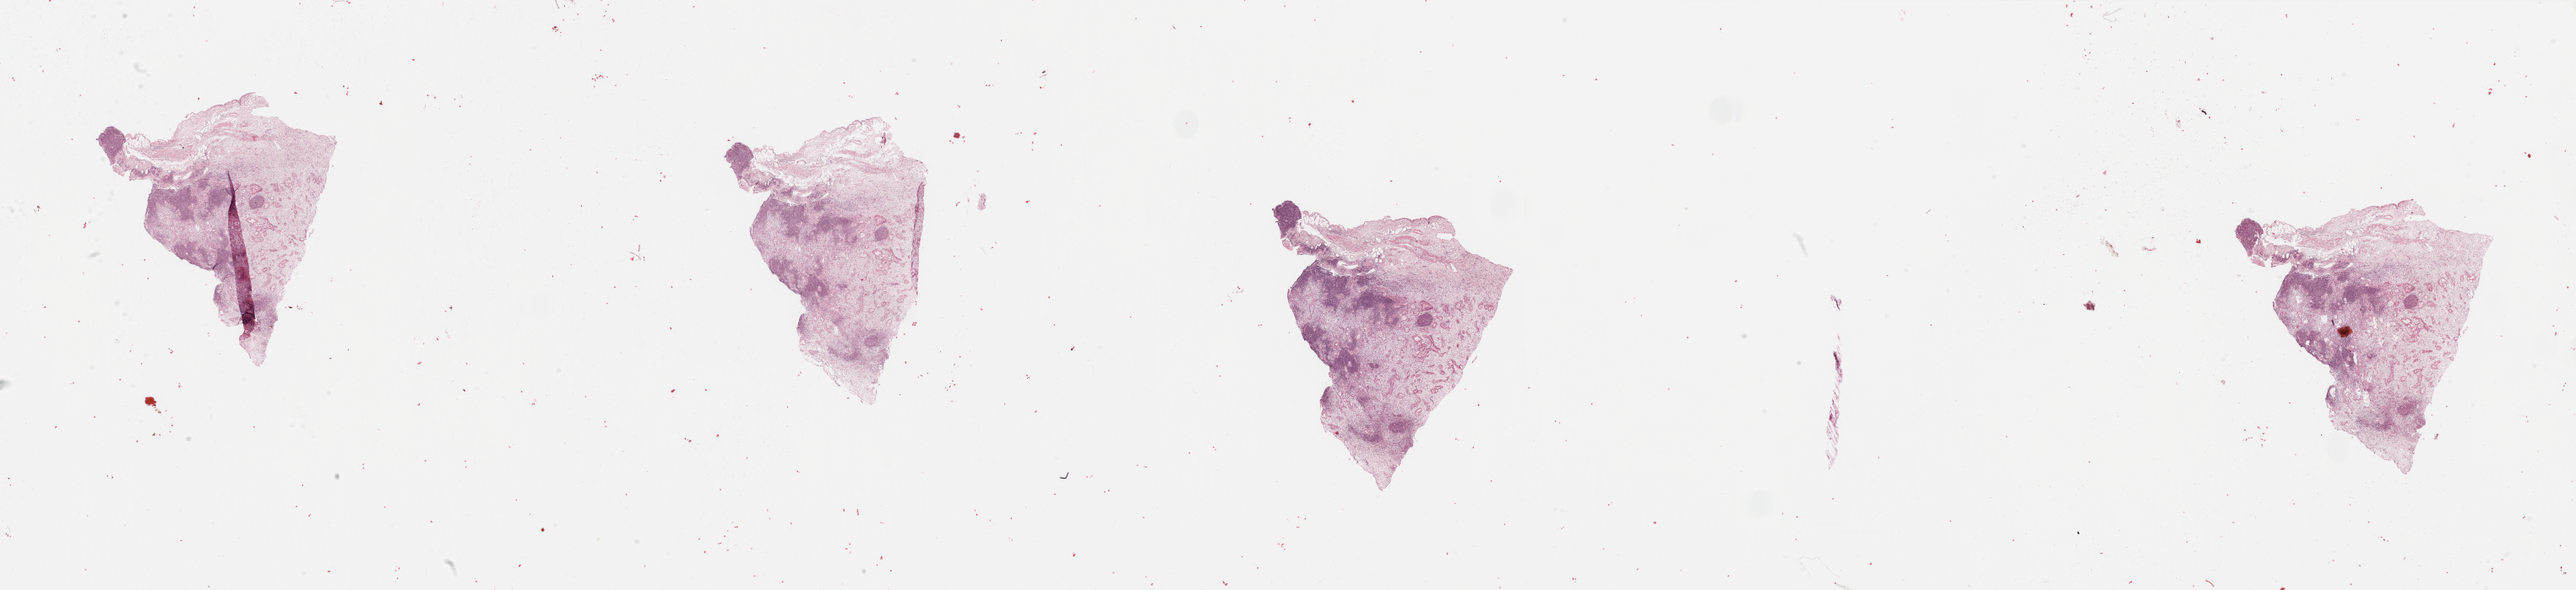
H&E-stained whole-slide image — a low-resolution overview of the entire scanned area, about 48.2 x 11.1 mm (slide scanned at 20x), tumour tissue sample, sampled site: pancreas. Patient: male, age 63 years. Histologic grade: G2 (moderately differentiated). Composition of this section per pathologist review: tumour nuclei 20%, necrosis 0%.
Primary tumour site (as recorded): head. Diagnosis: Infiltrating duct carcinoma, NOS.